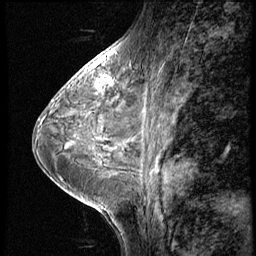
Breast MRI (dynamic contrast-enhanced), one sagittal slice. 4 images stored at this slice position (order not interpretable as contrast timing). 1.5 T. TE 4.2 ms, TR 8.9 ms. 256 × 256 image matrix. Female patient, age 38 years. From the clinical record (not read from this slice): setting: breast cancer imaged before/during neoadjuvant chemotherapy; receptor status: triple-negative.
Annotated regions visible in this slice (semi-automatic segmentation, software-assisted and operator-edited):
- analysis volume of interest (the breast-tissue region the enhancement analysis was run in; not a lesion): bounding box (x1, y1, x2, y2) in pixels: (88, 73, 115, 102)
- tumour enhancement mask (voxels above the 140 % enhancement threshold inside the analysis volume of interest): (95, 76, 113, 91)